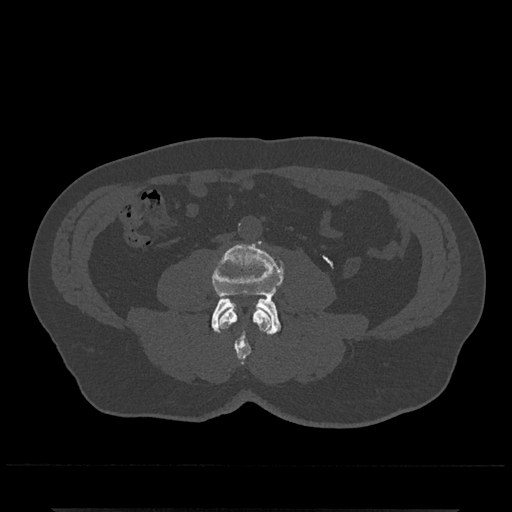
CT including the spine, one axial slice; position 183 of 797 along the scan axis; reconstruction kernel Br40s/3; bone window (W 1800 / L 400 HU); 0.5 mm slice thickness; 512 × 512 image matrix, field of view 393 × 393 mm. Patient: male, 67 years. Case-level facts recorded for this patient, not image findings: primary cancer: prostate.
Structures marked on this image (semi-automatic segmentation, software-assisted and operator-edited):
- L3 vertebra: bounding box (x1, y1, x2, y2) in pixels: (218, 307, 272, 365)
- L4 vertebra: (211, 242, 284, 335)